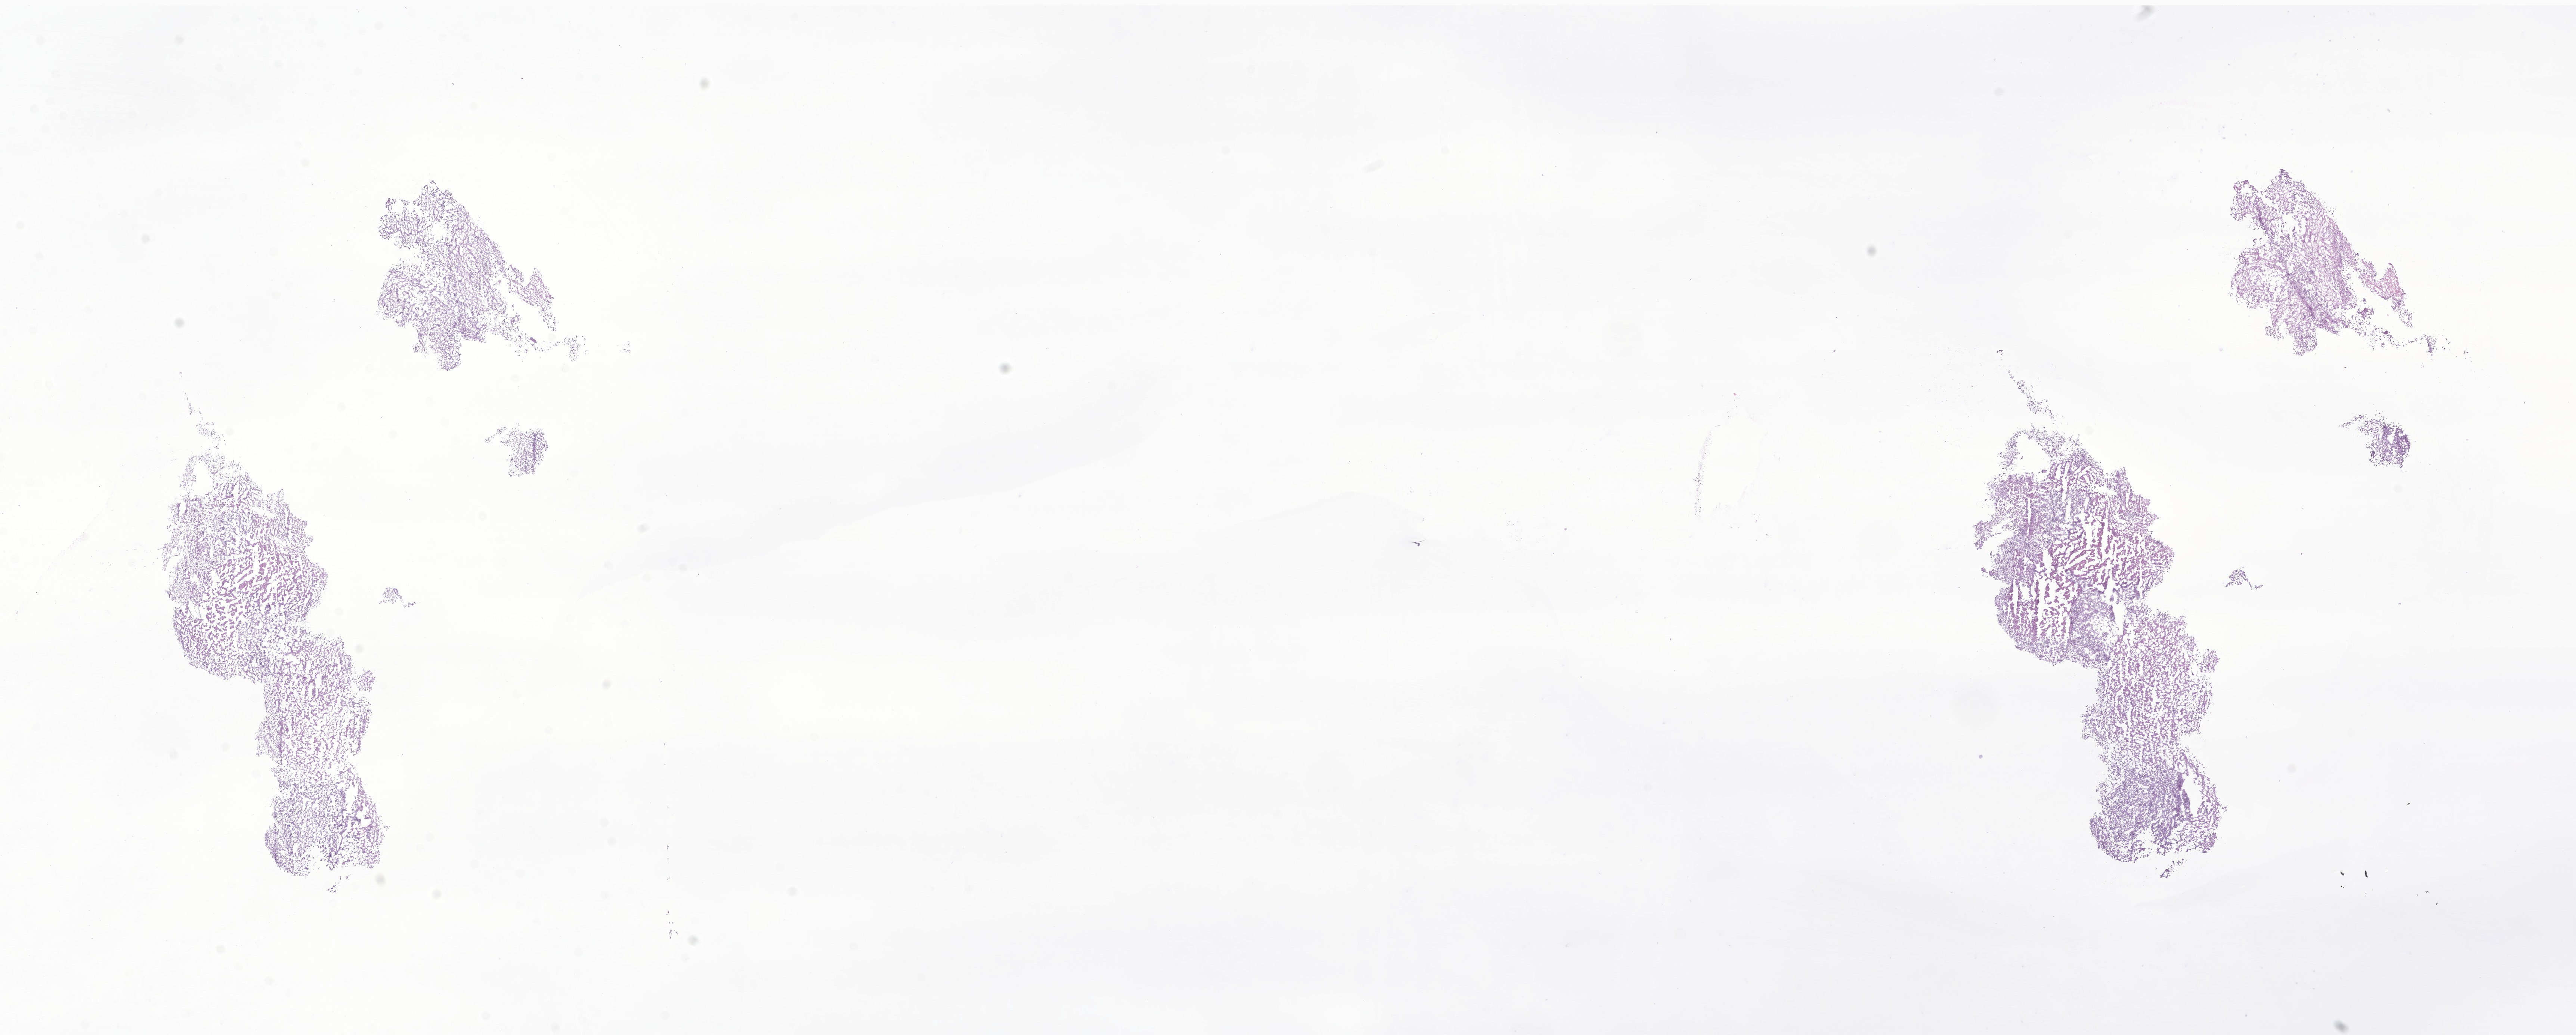
Digitized haematoxylin and eosin-stained section of tumor tissue from the frontal lobe — low-resolution overview of the scanned area, about 29.1 x 11.7 mm, frozen section (OCT-embedded). Female patient, age 742 days (about 2.0 years).
* recorded diagnosis: Atypical teratoid/rhabdoid tumor